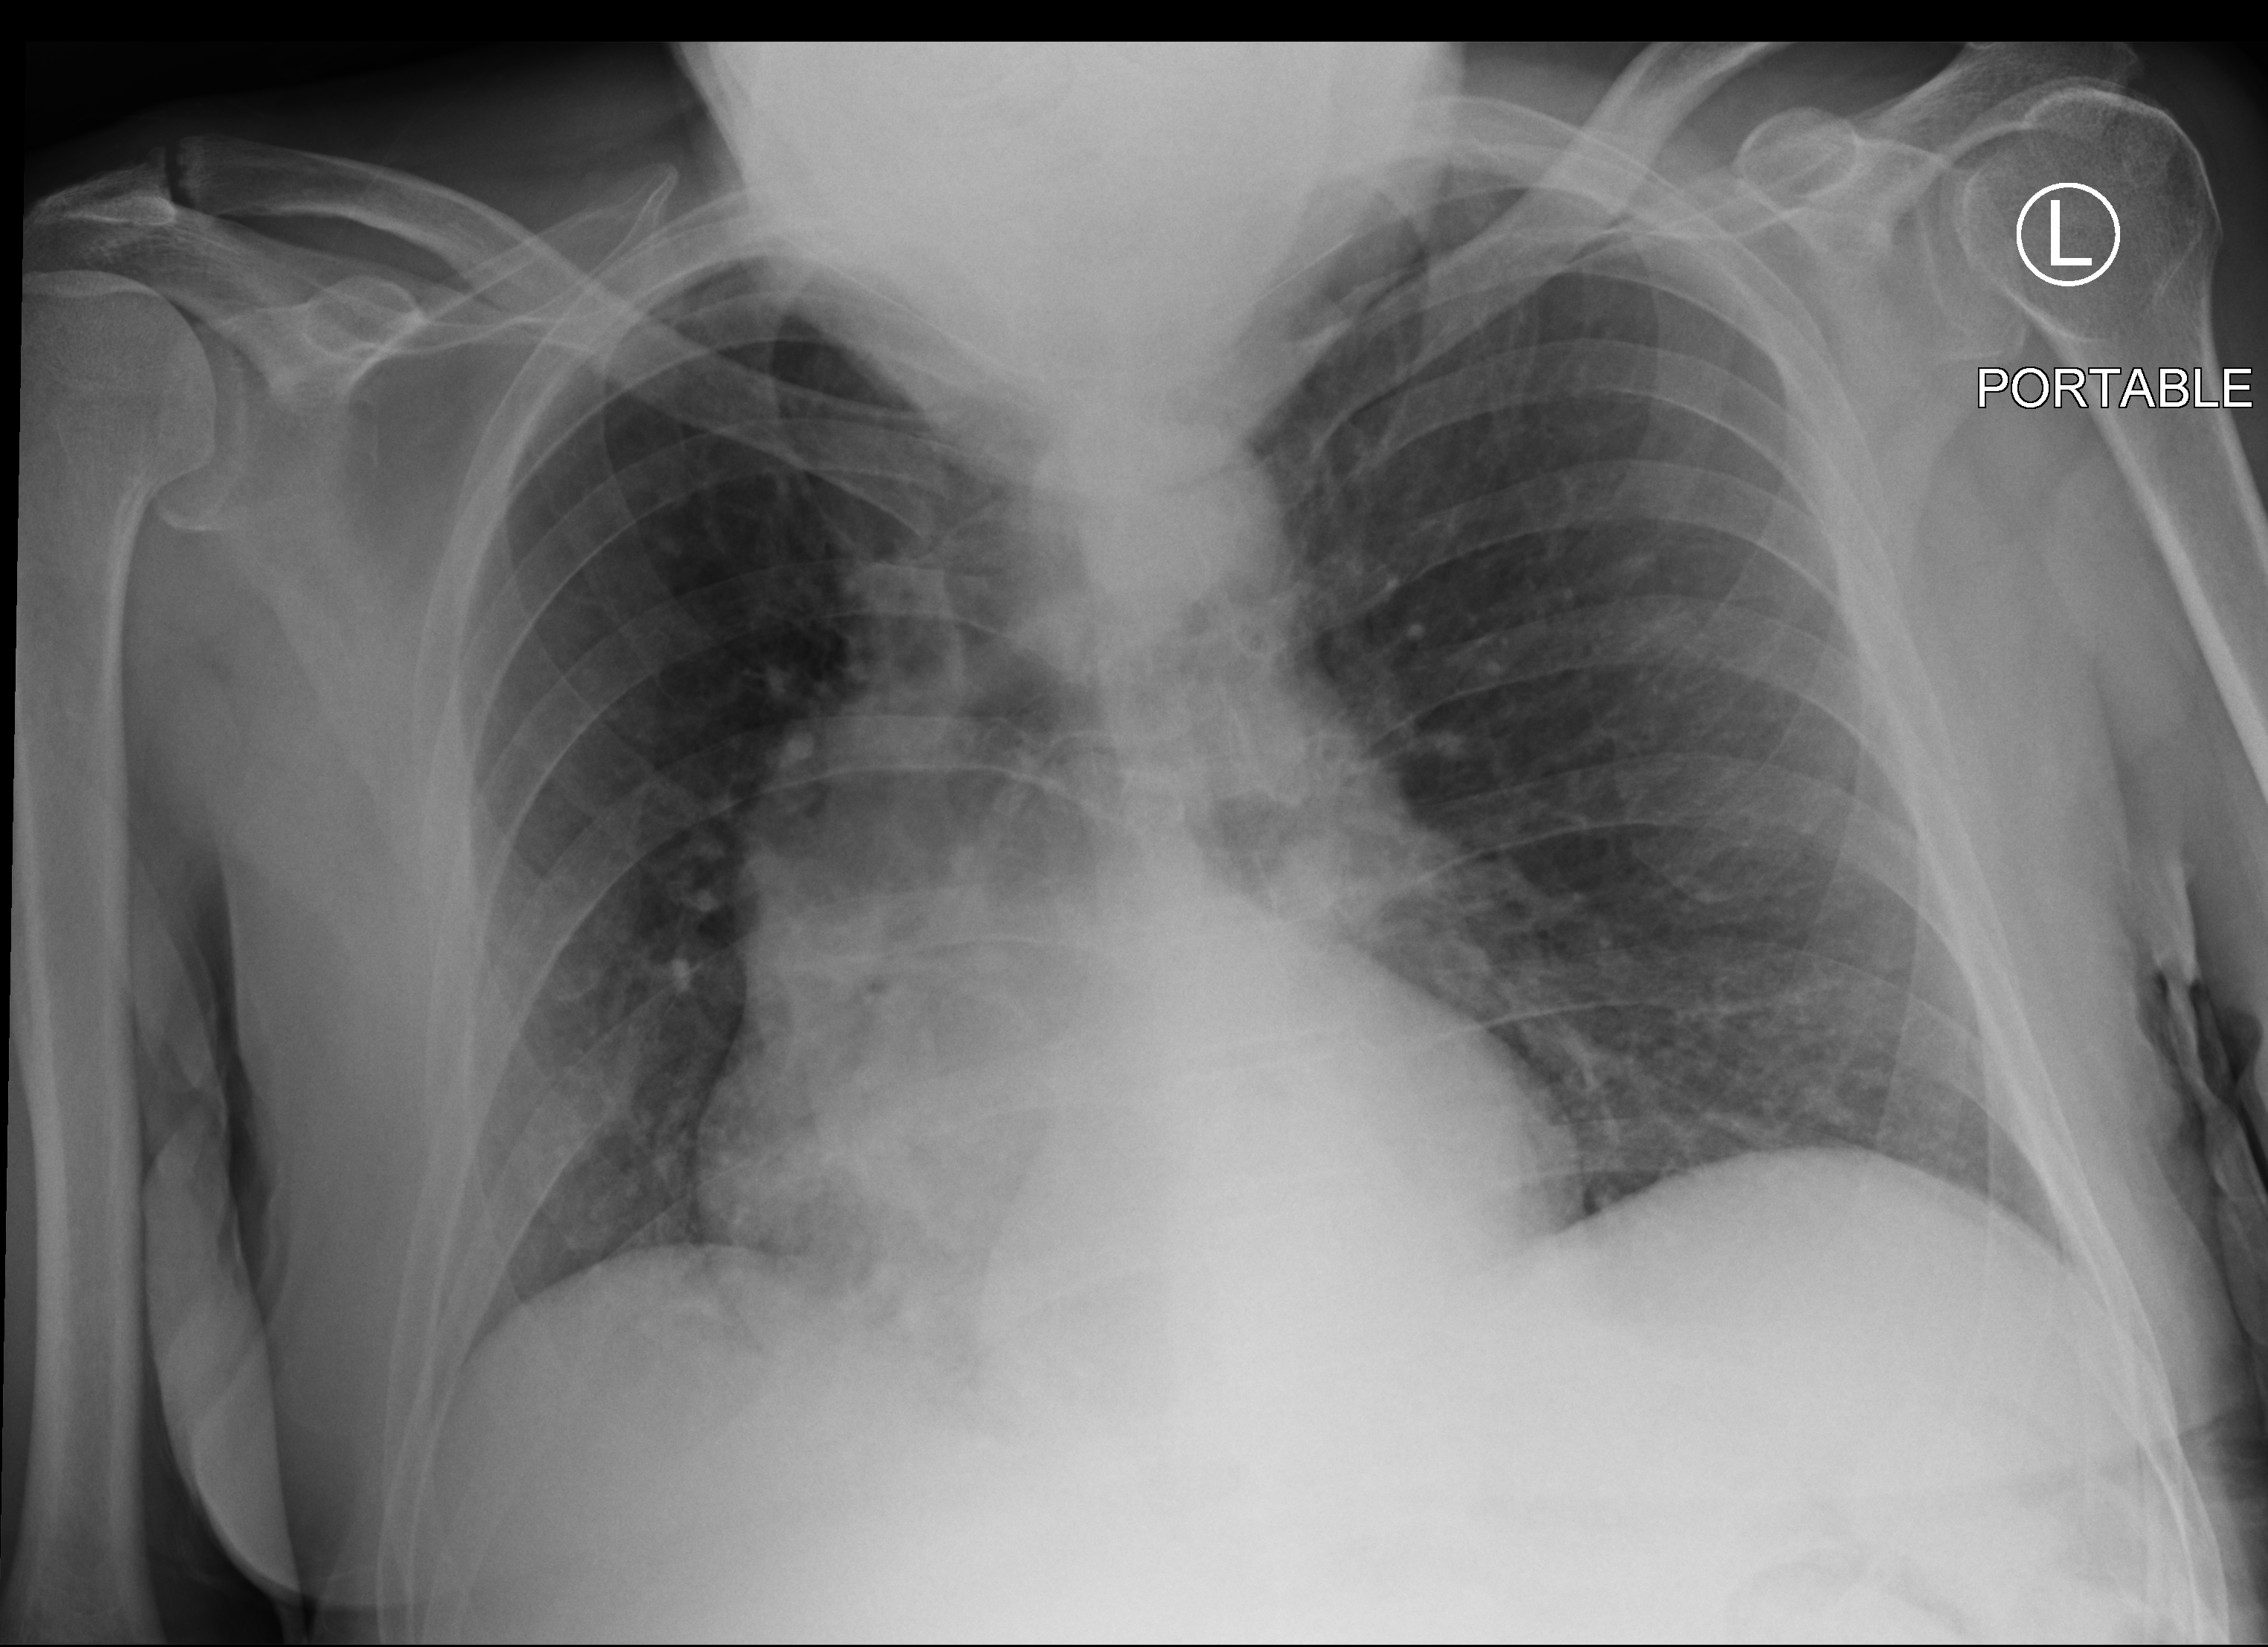
Chest X-ray (portable), anteroposterior (AP) projection. Patient hospitalised with COVID-19; male, aged 60–74 years.
Hospital-stay facts (about this admission, not read from this image; timing relative to this image not recorded): mechanically ventilated during this hospital stay: no.